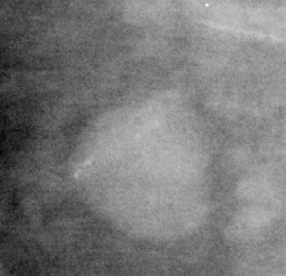
Crop from a digitized film mammogram around one marked abnormality; right breast; MLO view; BI-RADS breast density category 1 (scale 1–4).
- Marked abnormality: mass, shape oval, margins circumscribed; BI-RADS assessment category 3; subtlety rating 5 on a 1 (subtle) to 5 (obvious) scale; pathology (as recorded): benign.